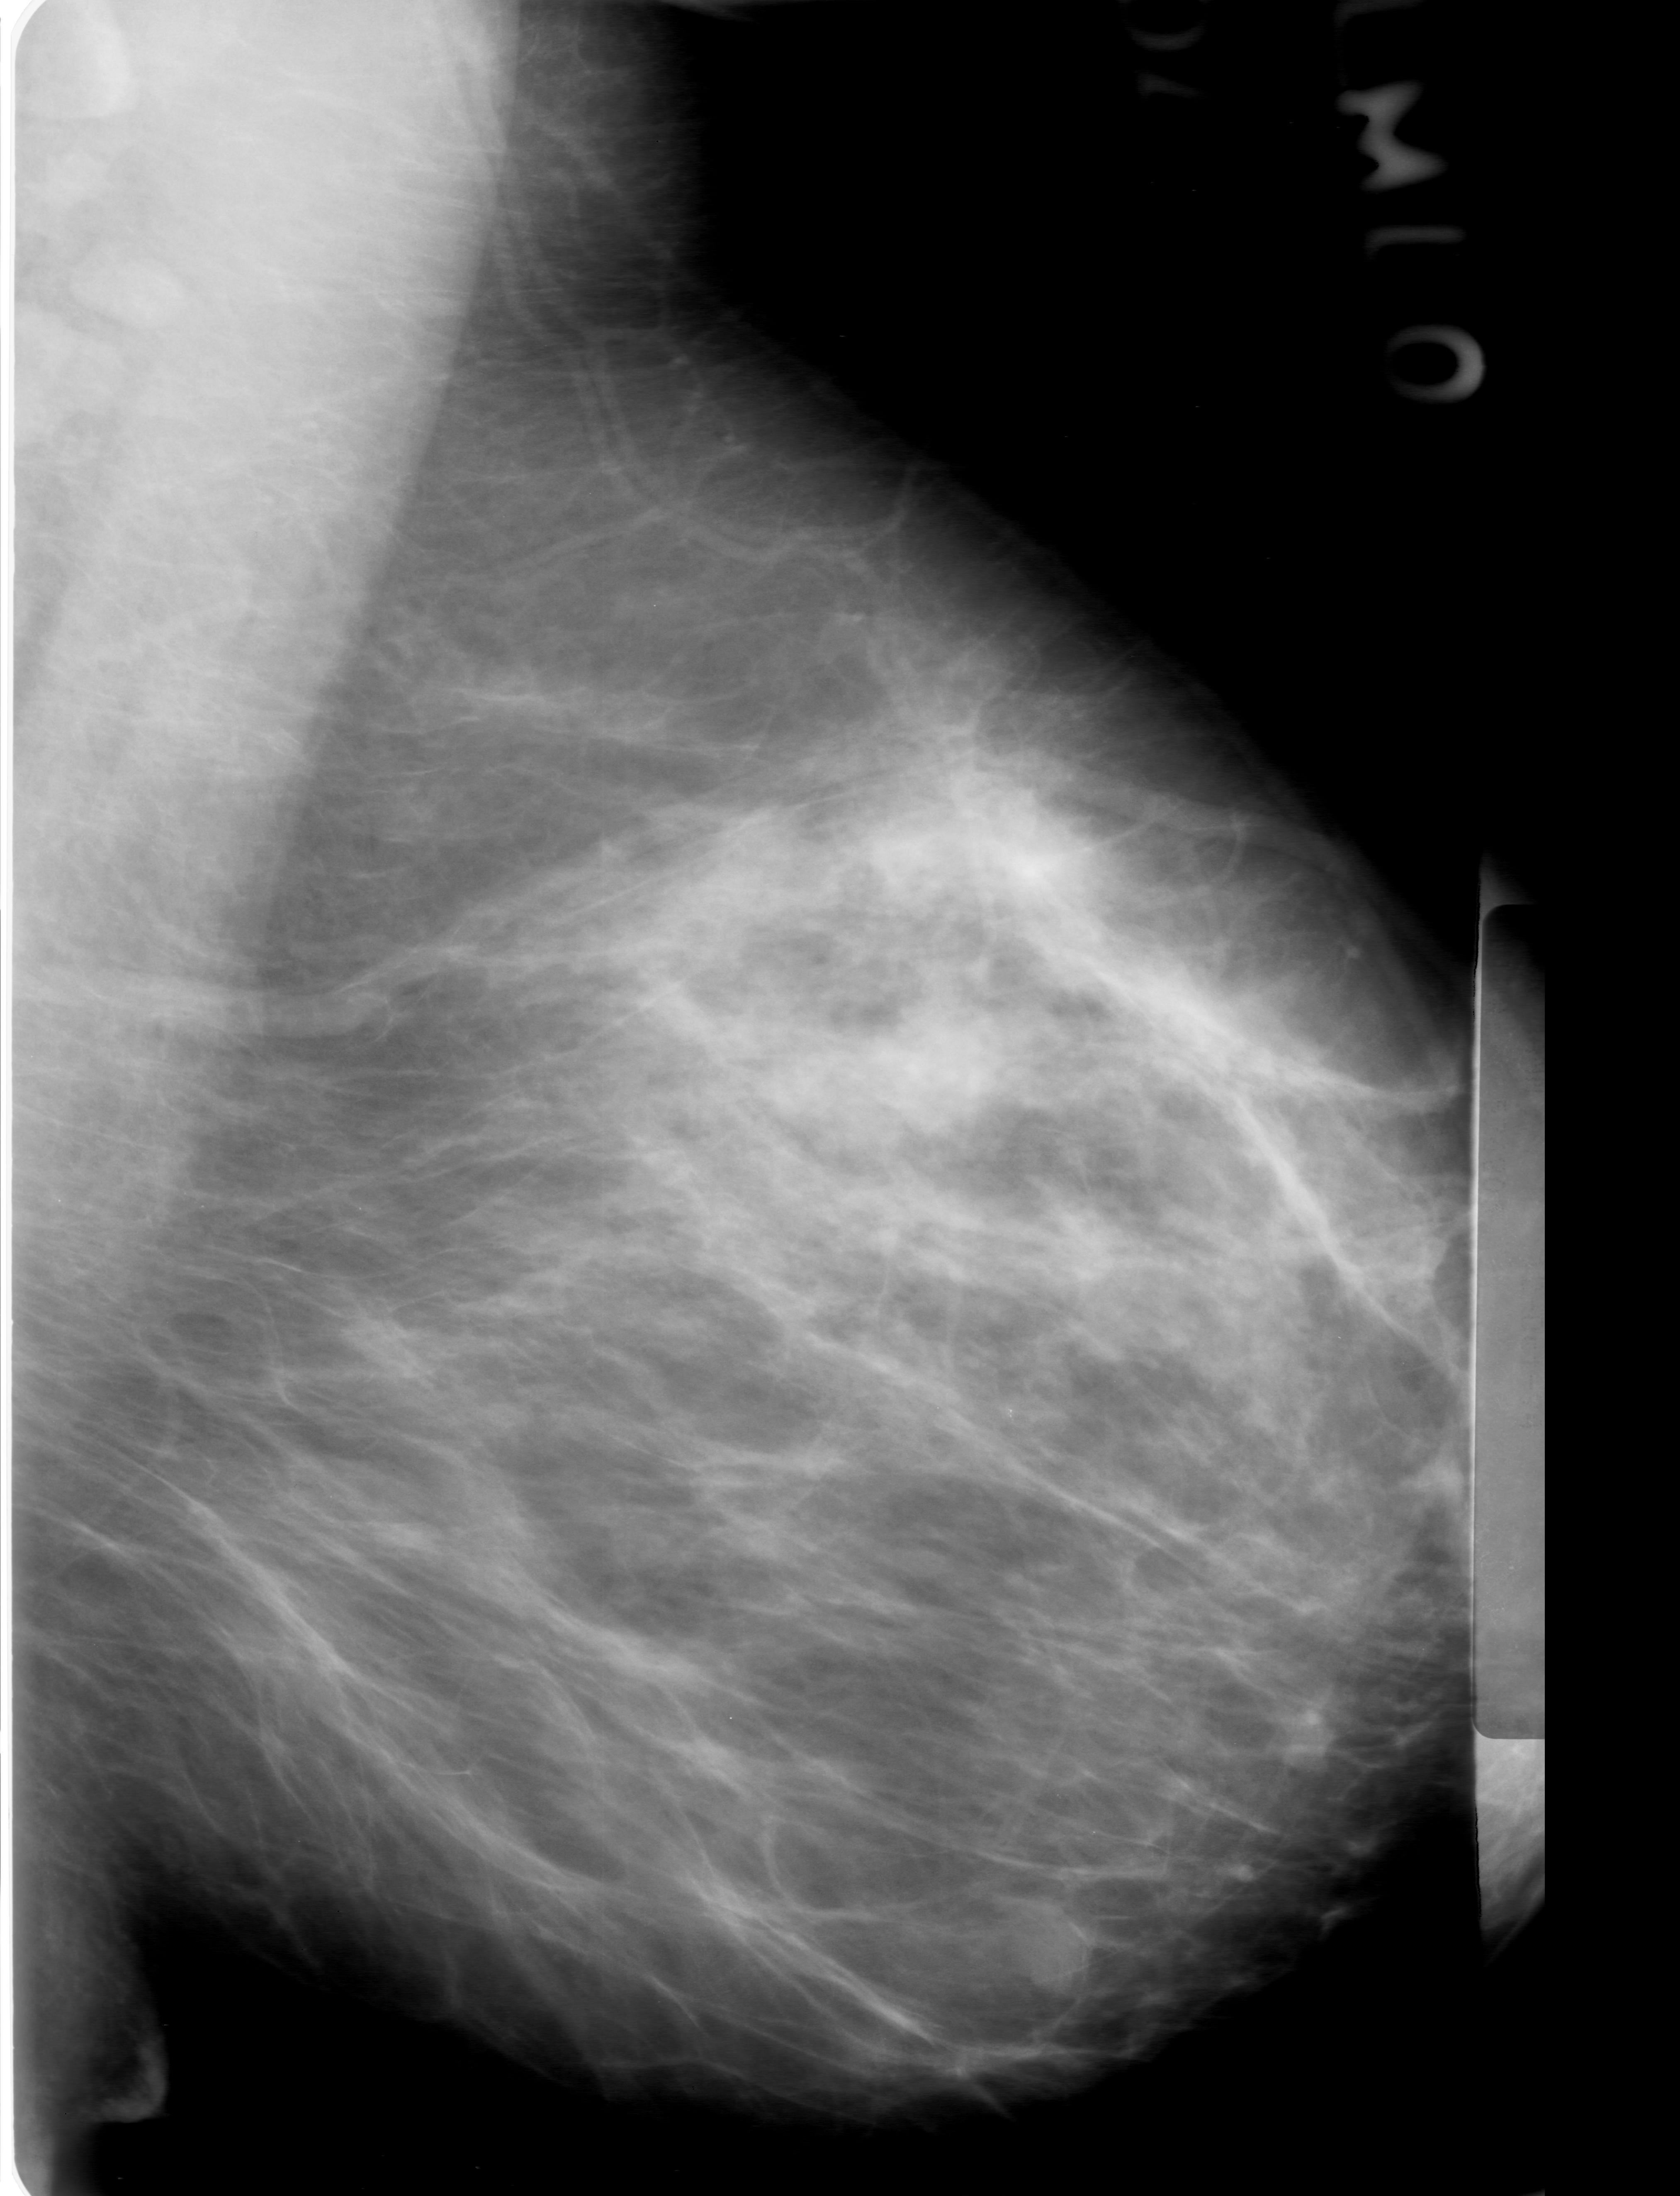
Digitized screen-film mammogram. Left breast. MLO view. Breast composition: heterogeneously dense (BI-RADS density category 3 of 4). 1680 × 2196 image matrix.
Marked abnormalities (boxes around the expert regions of interest):
- mass, shape oval, margins obscured; BI-RADS assessment category 0 (incomplete: needs additional imaging); pathology (as recorded): benign: bounding box [x1, y1, x2, y2] px = [972, 1891, 1124, 2010]